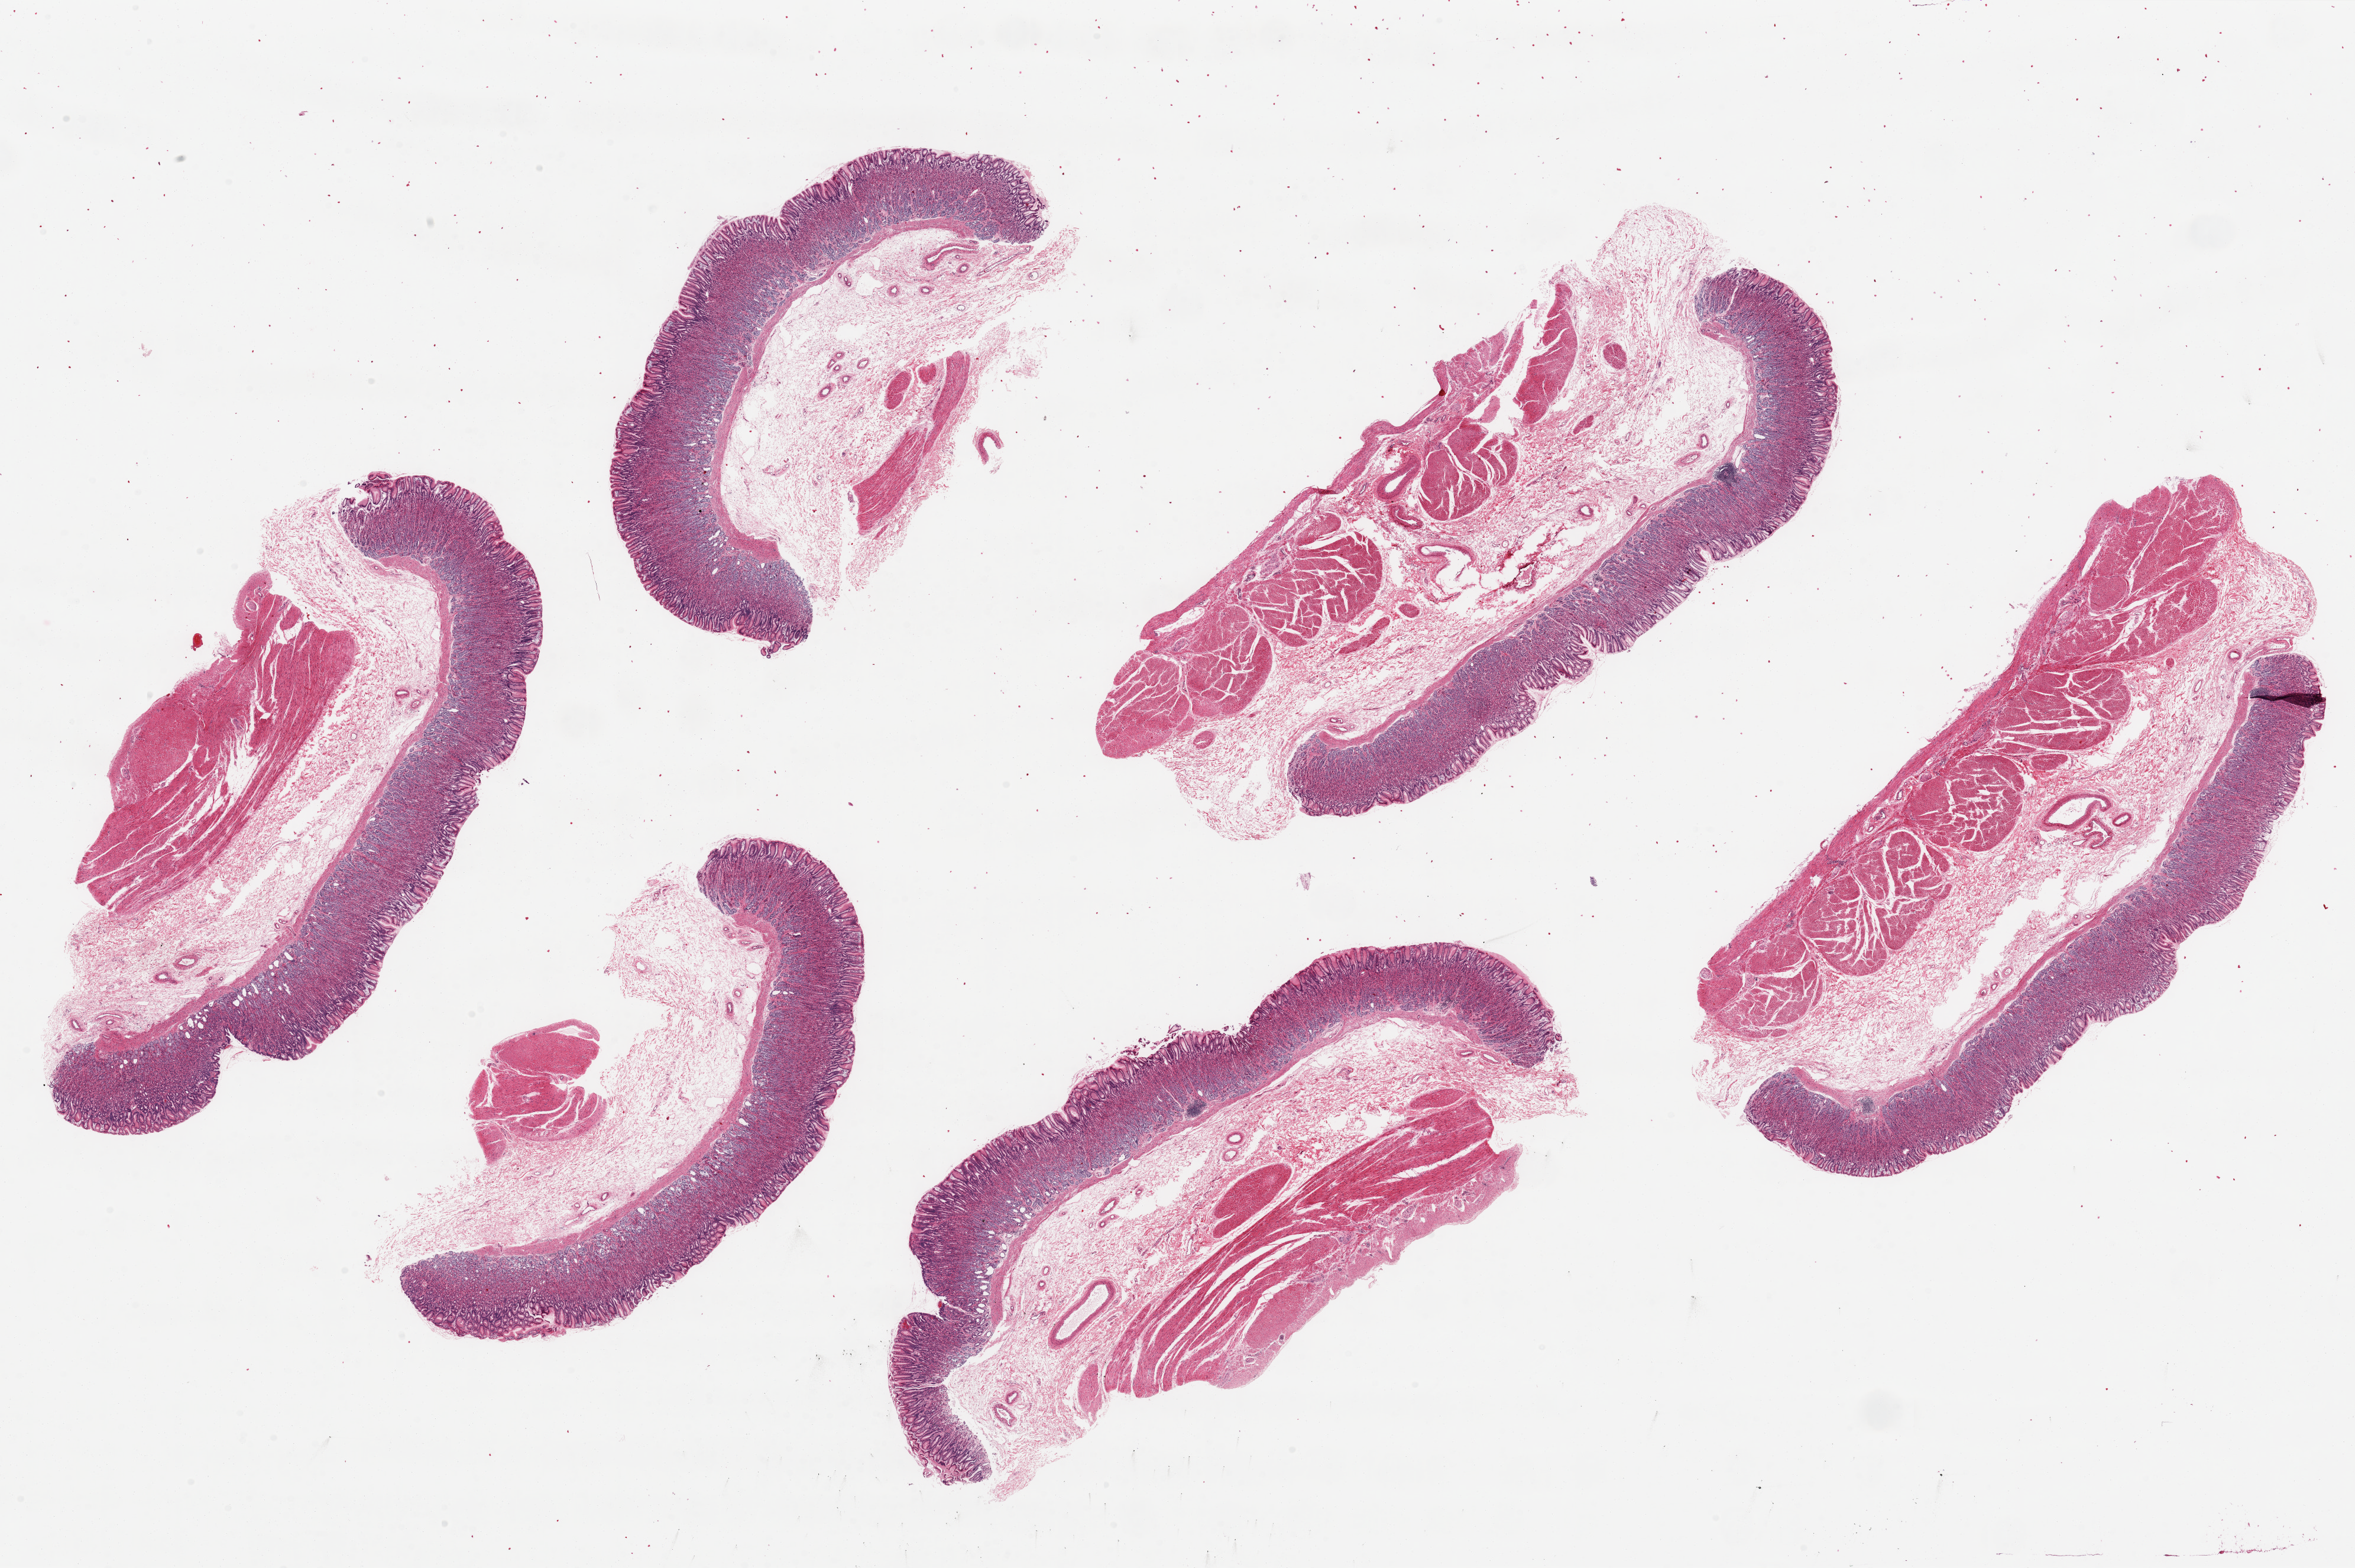
Digitized H&E-stained section, brightfield — shown as a low-resolution overview of the whole scanned area (about 31.5 x 21.0 mm); PAXgene-fixed, paraffin-embedded tissue; section of stomach (target tissue); tissue donor sample. Donor: female.
Pathologist's review note for this sample: 6 pieces, ~ 10x4mm. Mucosa extremely well preserved, ~30% of thickness.